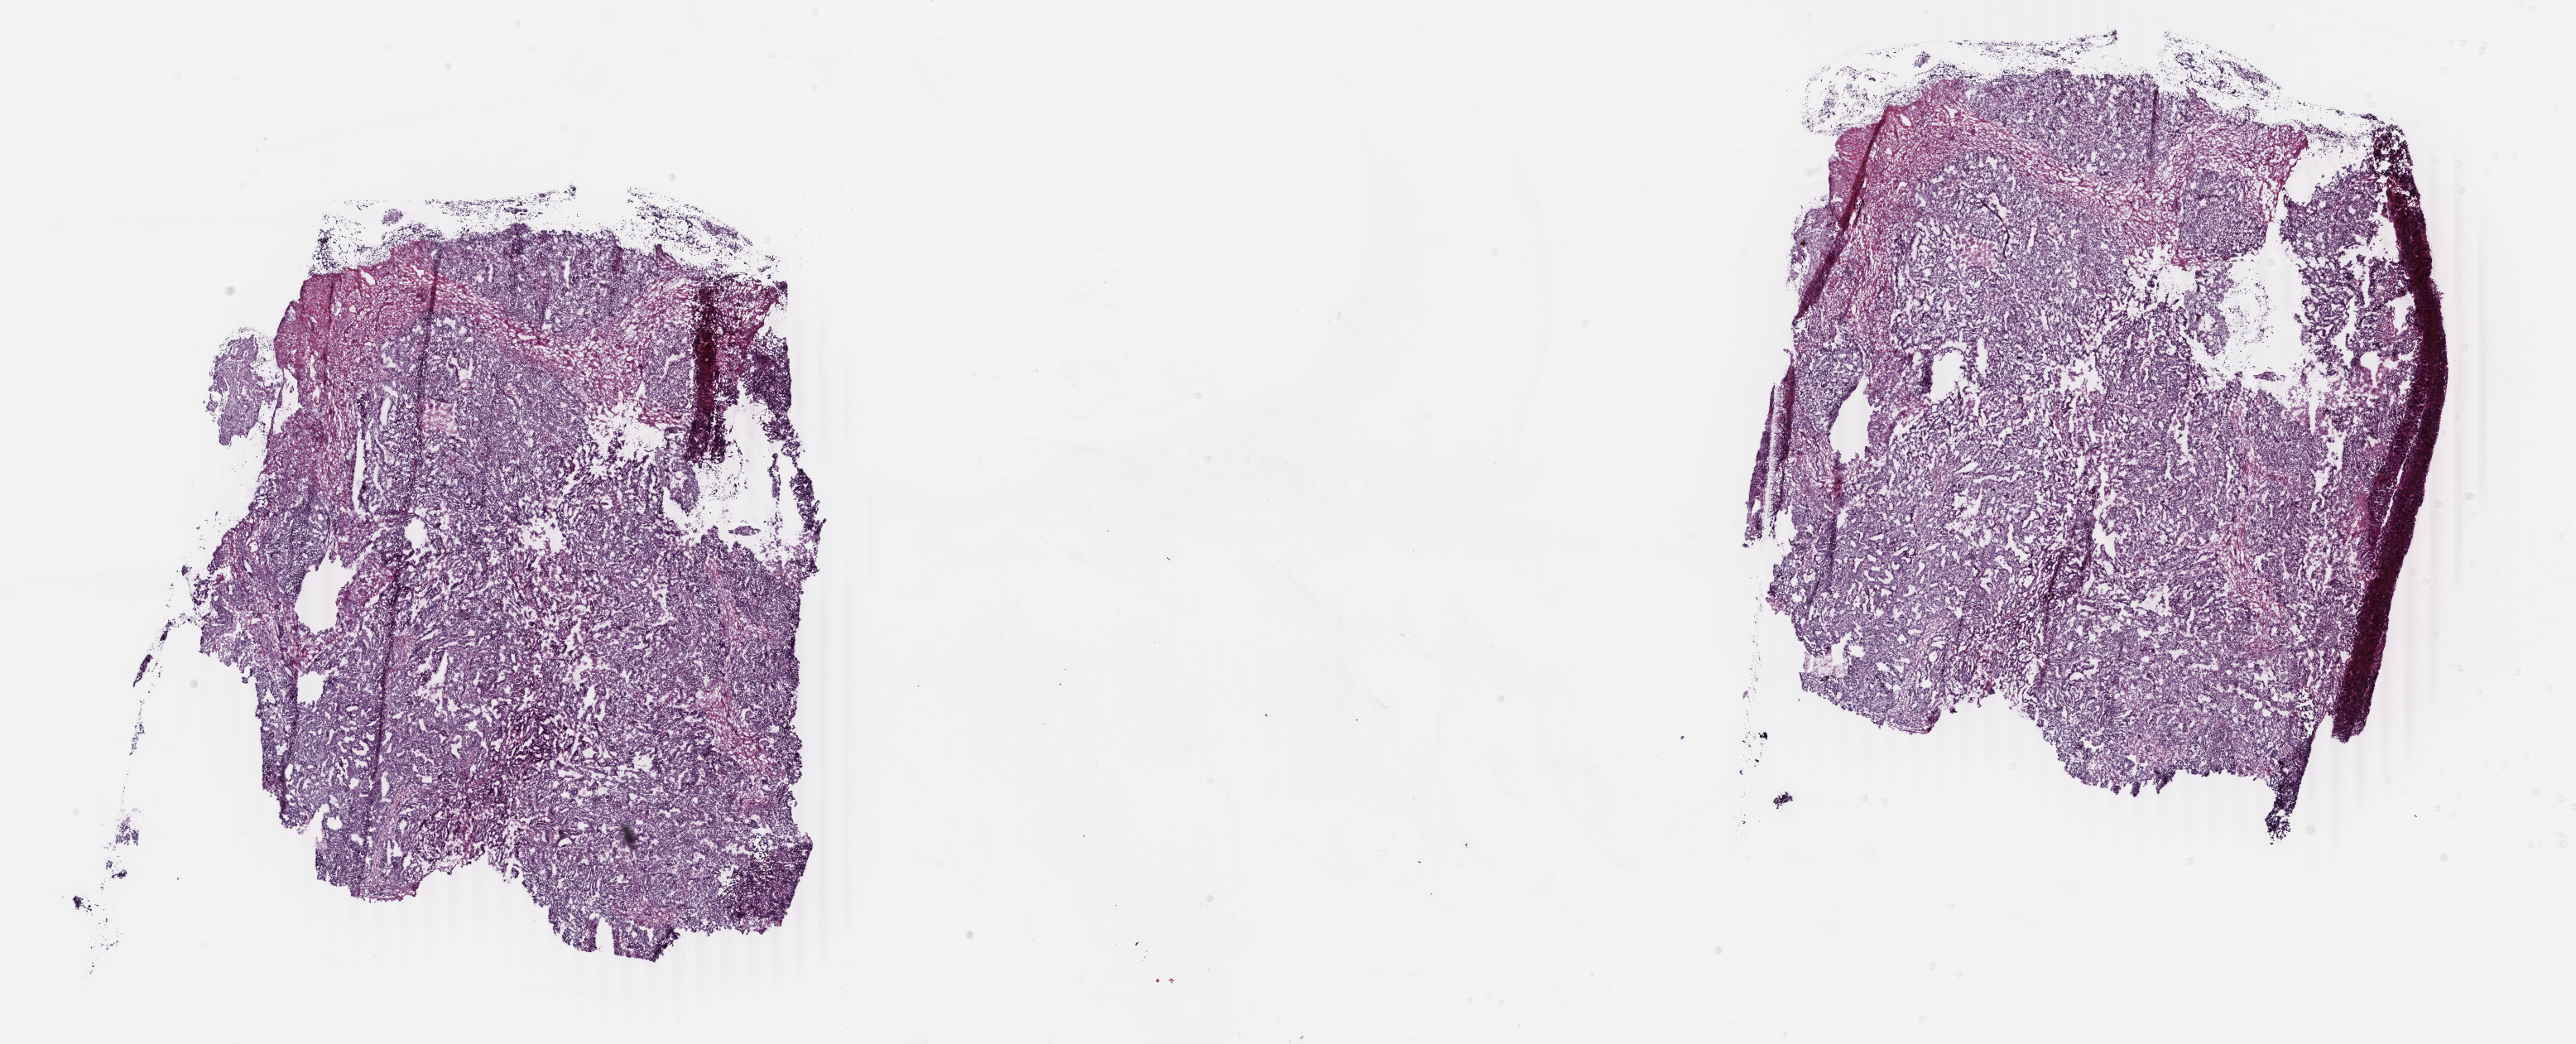
Whole-slide histology image, H&E, shown as a low-resolution overview of the whole scanned area (about 24.7 x 10.0 mm); frozen section from the top of the tissue portion; primary tumour sample from the uterus. Female, age 53 years at initial diagnosis. Histologic grade: G1 (well differentiated). Composition of this section per pathologist review: tumour cells 80%, tumour nuclei 85%, normal cells 14%, stromal cells 1%, necrosis 5%. Inflammatory infiltration, as recorded: lymphocyte infiltration 1%, monocyte infiltration 0%, neutrophil infiltration 0%.
• FIGO stage: IB
• histologic diagnosis: Endometrioid adenocarcinoma, NOS